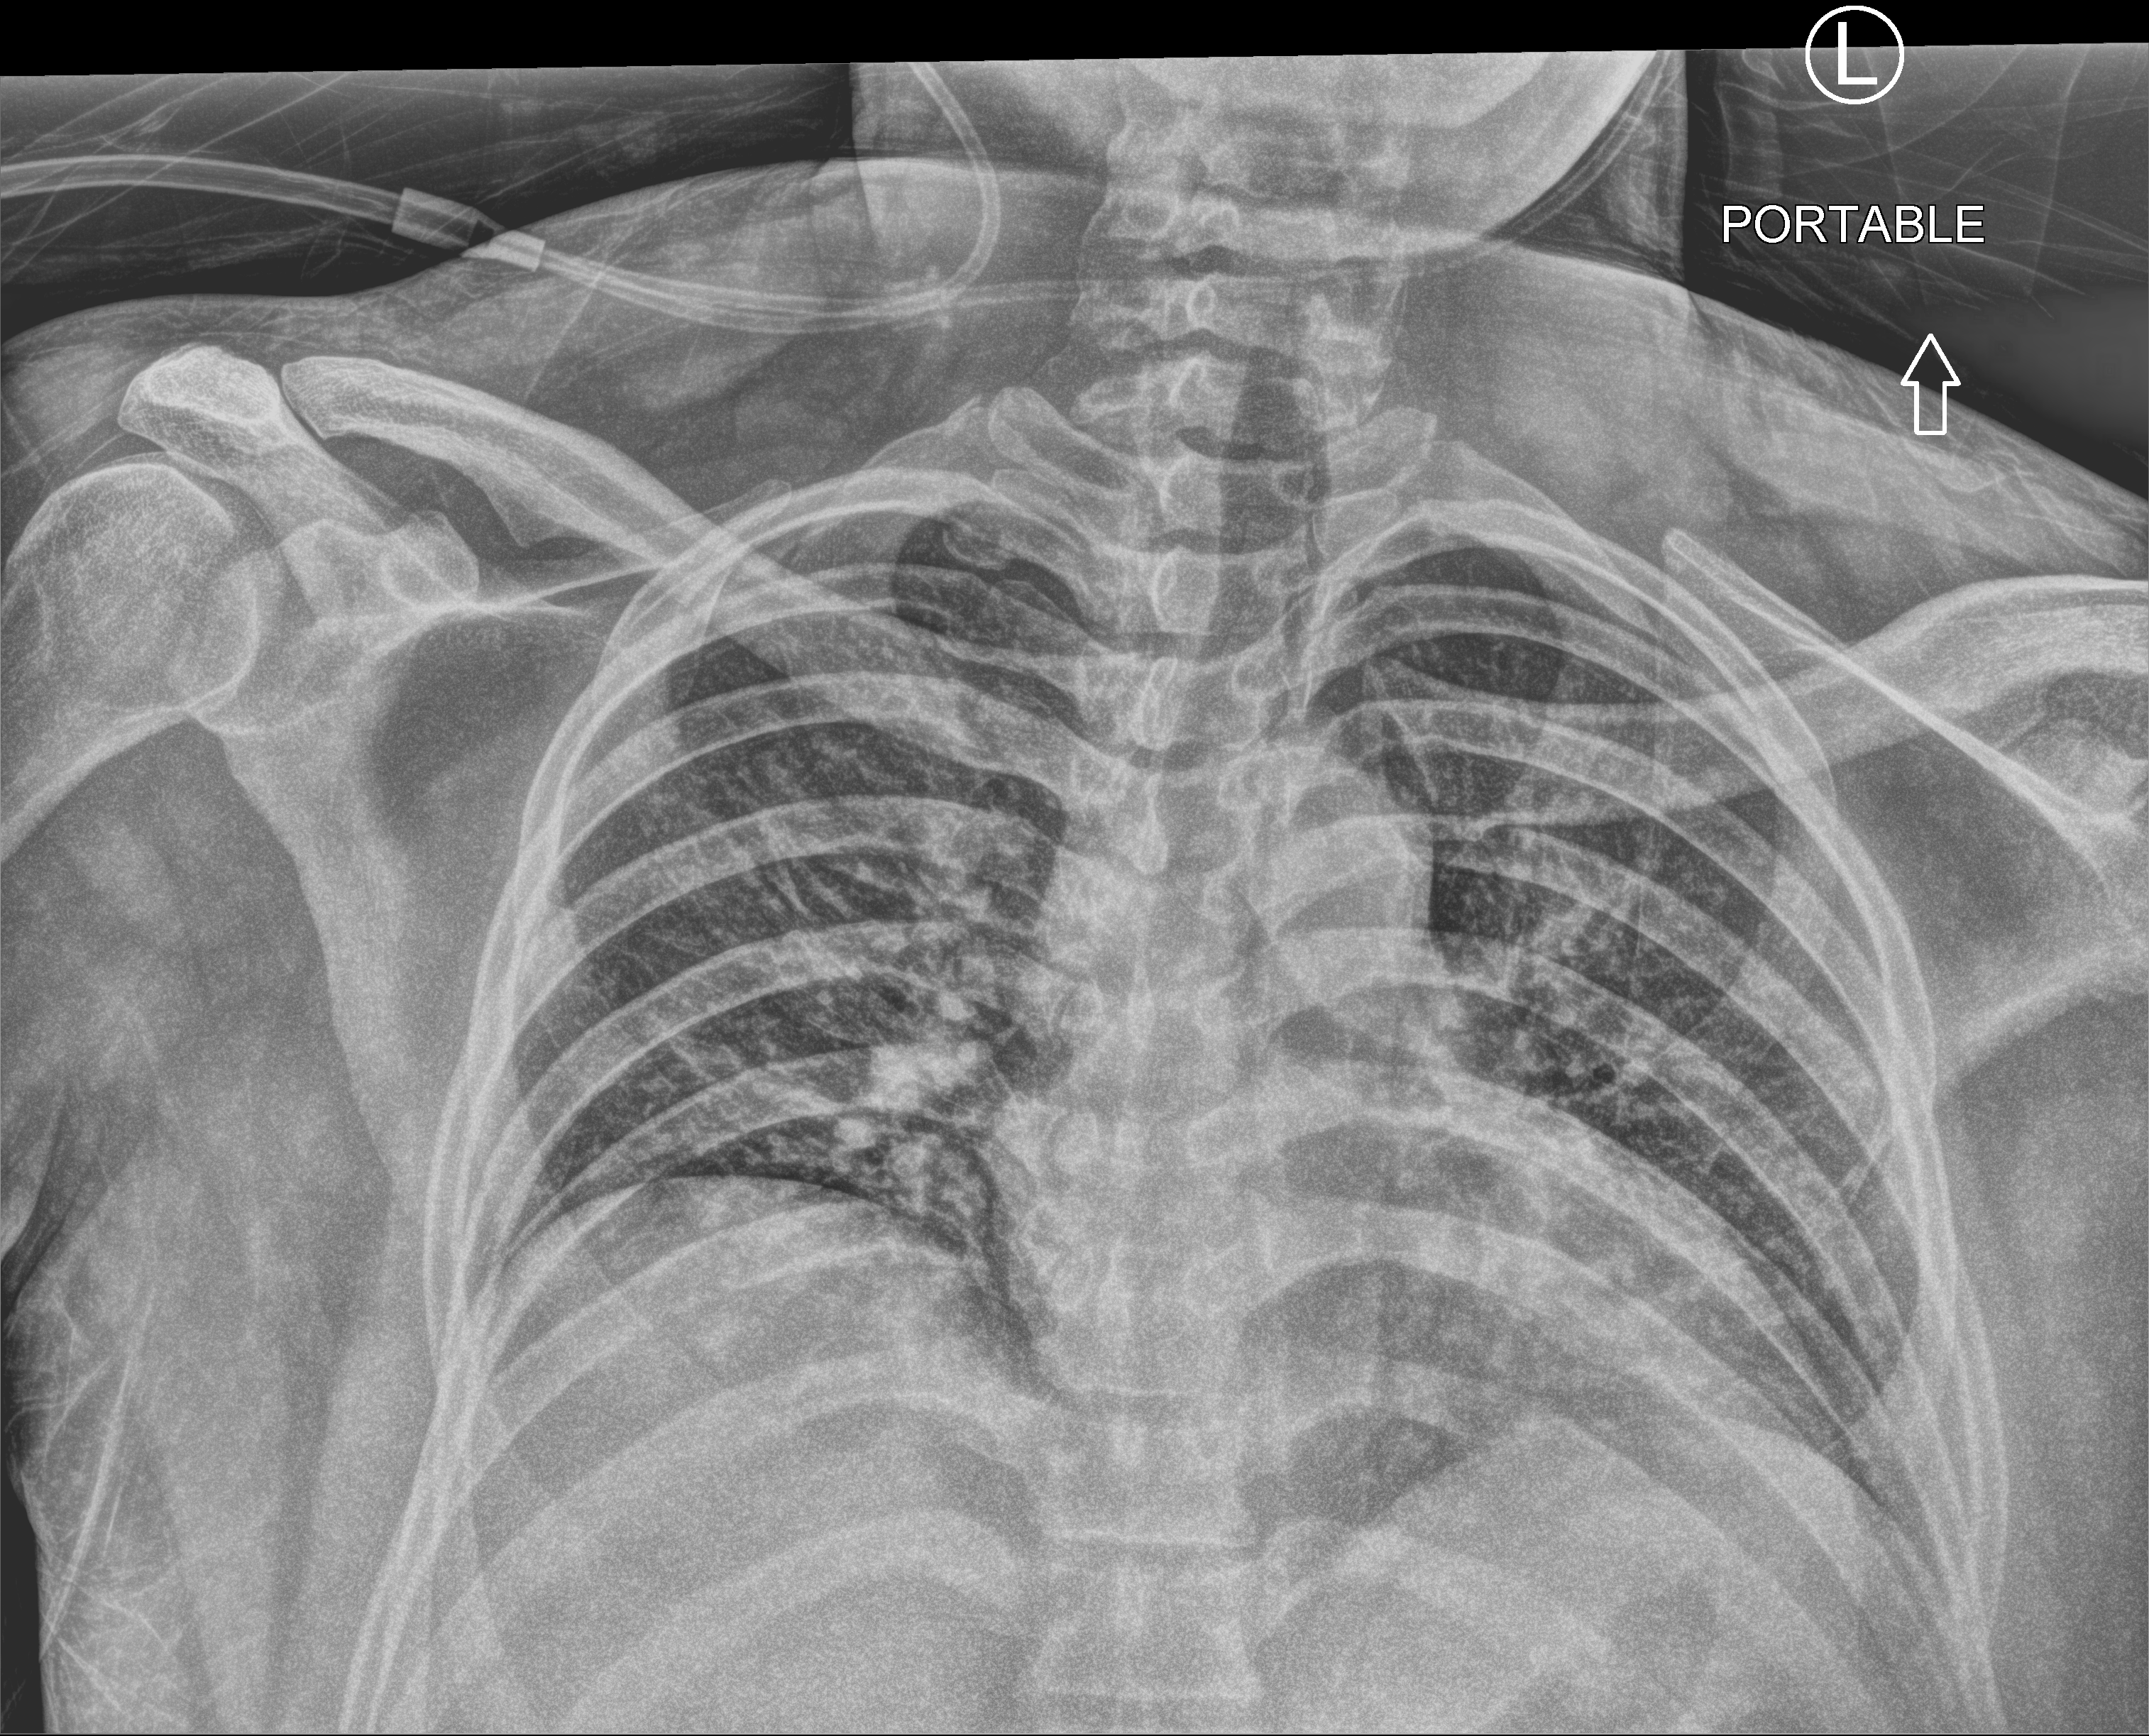
Bedside chest radiograph (computed radiography); anteroposterior (AP) projection. Patient hospitalised with COVID-19; male, aged 18–59 years.
Hospital-stay facts (about this admission, not read from this image; timing relative to this image not recorded): mechanically ventilated during this hospital stay: no; diabetes (admission record): no.